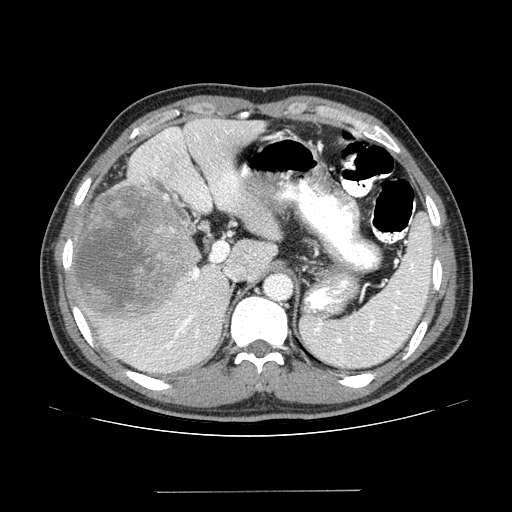
Contrast-enhanced abdominal CT (liver protocol), one axial slice. Reconstruction kernel STANDARD. 100 kVp. One of 2 acquisitions stored at this slice position. Soft-tissue window (W 400 / L 40 HU). 2.5 mm slice thickness. 512 × 512 image matrix, field of view 380 × 380 mm. From the clinical record (not read from this slice): diagnosis: hepatocellular carcinoma (patient treated with transarterial chemoembolisation; whether this scan precedes or follows treatment is not stated here); TNM stage (as recorded): Stage-I; Child-Pugh class: A; tumour differentiation: poorly differentiated; tumour nodularity: uninodular.
Annotated regions visible in this slice (semi-automatically segmented with operator editing):
- liver parenchyma outside the tumour (the mass and vessels are separate outlines, so this box may not span the whole liver): bounding box <66,118,266,372> (left, top, right, bottom; pixels)
- mass: <70,183,198,321>
- liver vessels: <68,129,232,368>